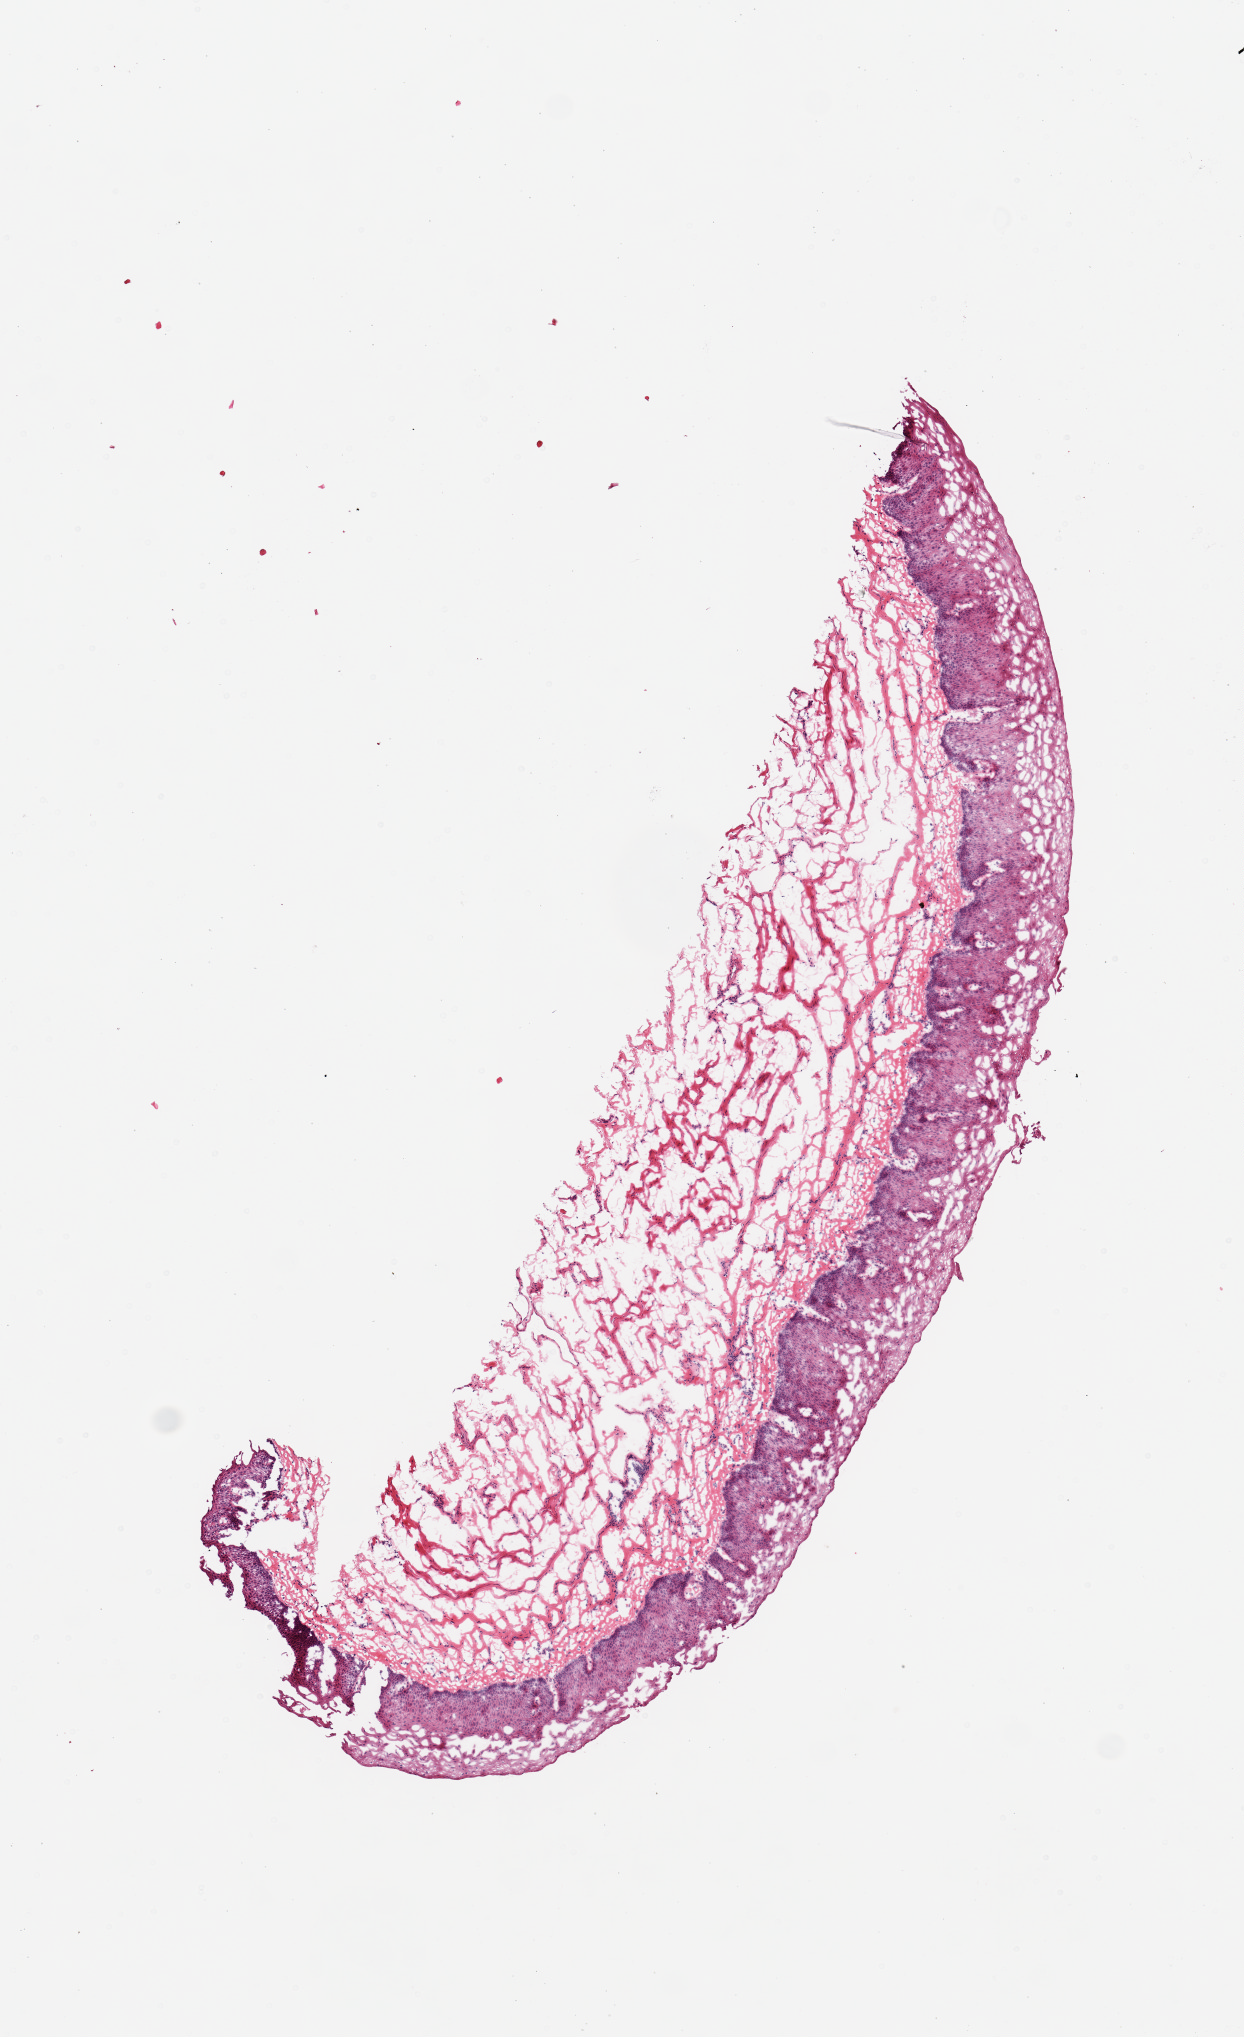
Digitized haematoxylin and eosin-stained section, brightfield — shown as a low-resolution overview of the whole scanned area (about 4.9 x 8.1 mm). Donor: male.
Specimen: frozen section; section of esophageal mucous membrane (target tissue); donor tissue sample.